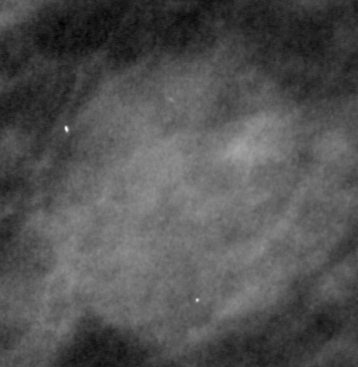
Region of interest cut from a scanned film mammogram (one marked finding), left breast, MLO view, BI-RADS breast density category 3 (scale 1–4).
- Mass, shape lobulated, margins ill defined; BI-RADS assessment category 4; pathology (as recorded): benign.